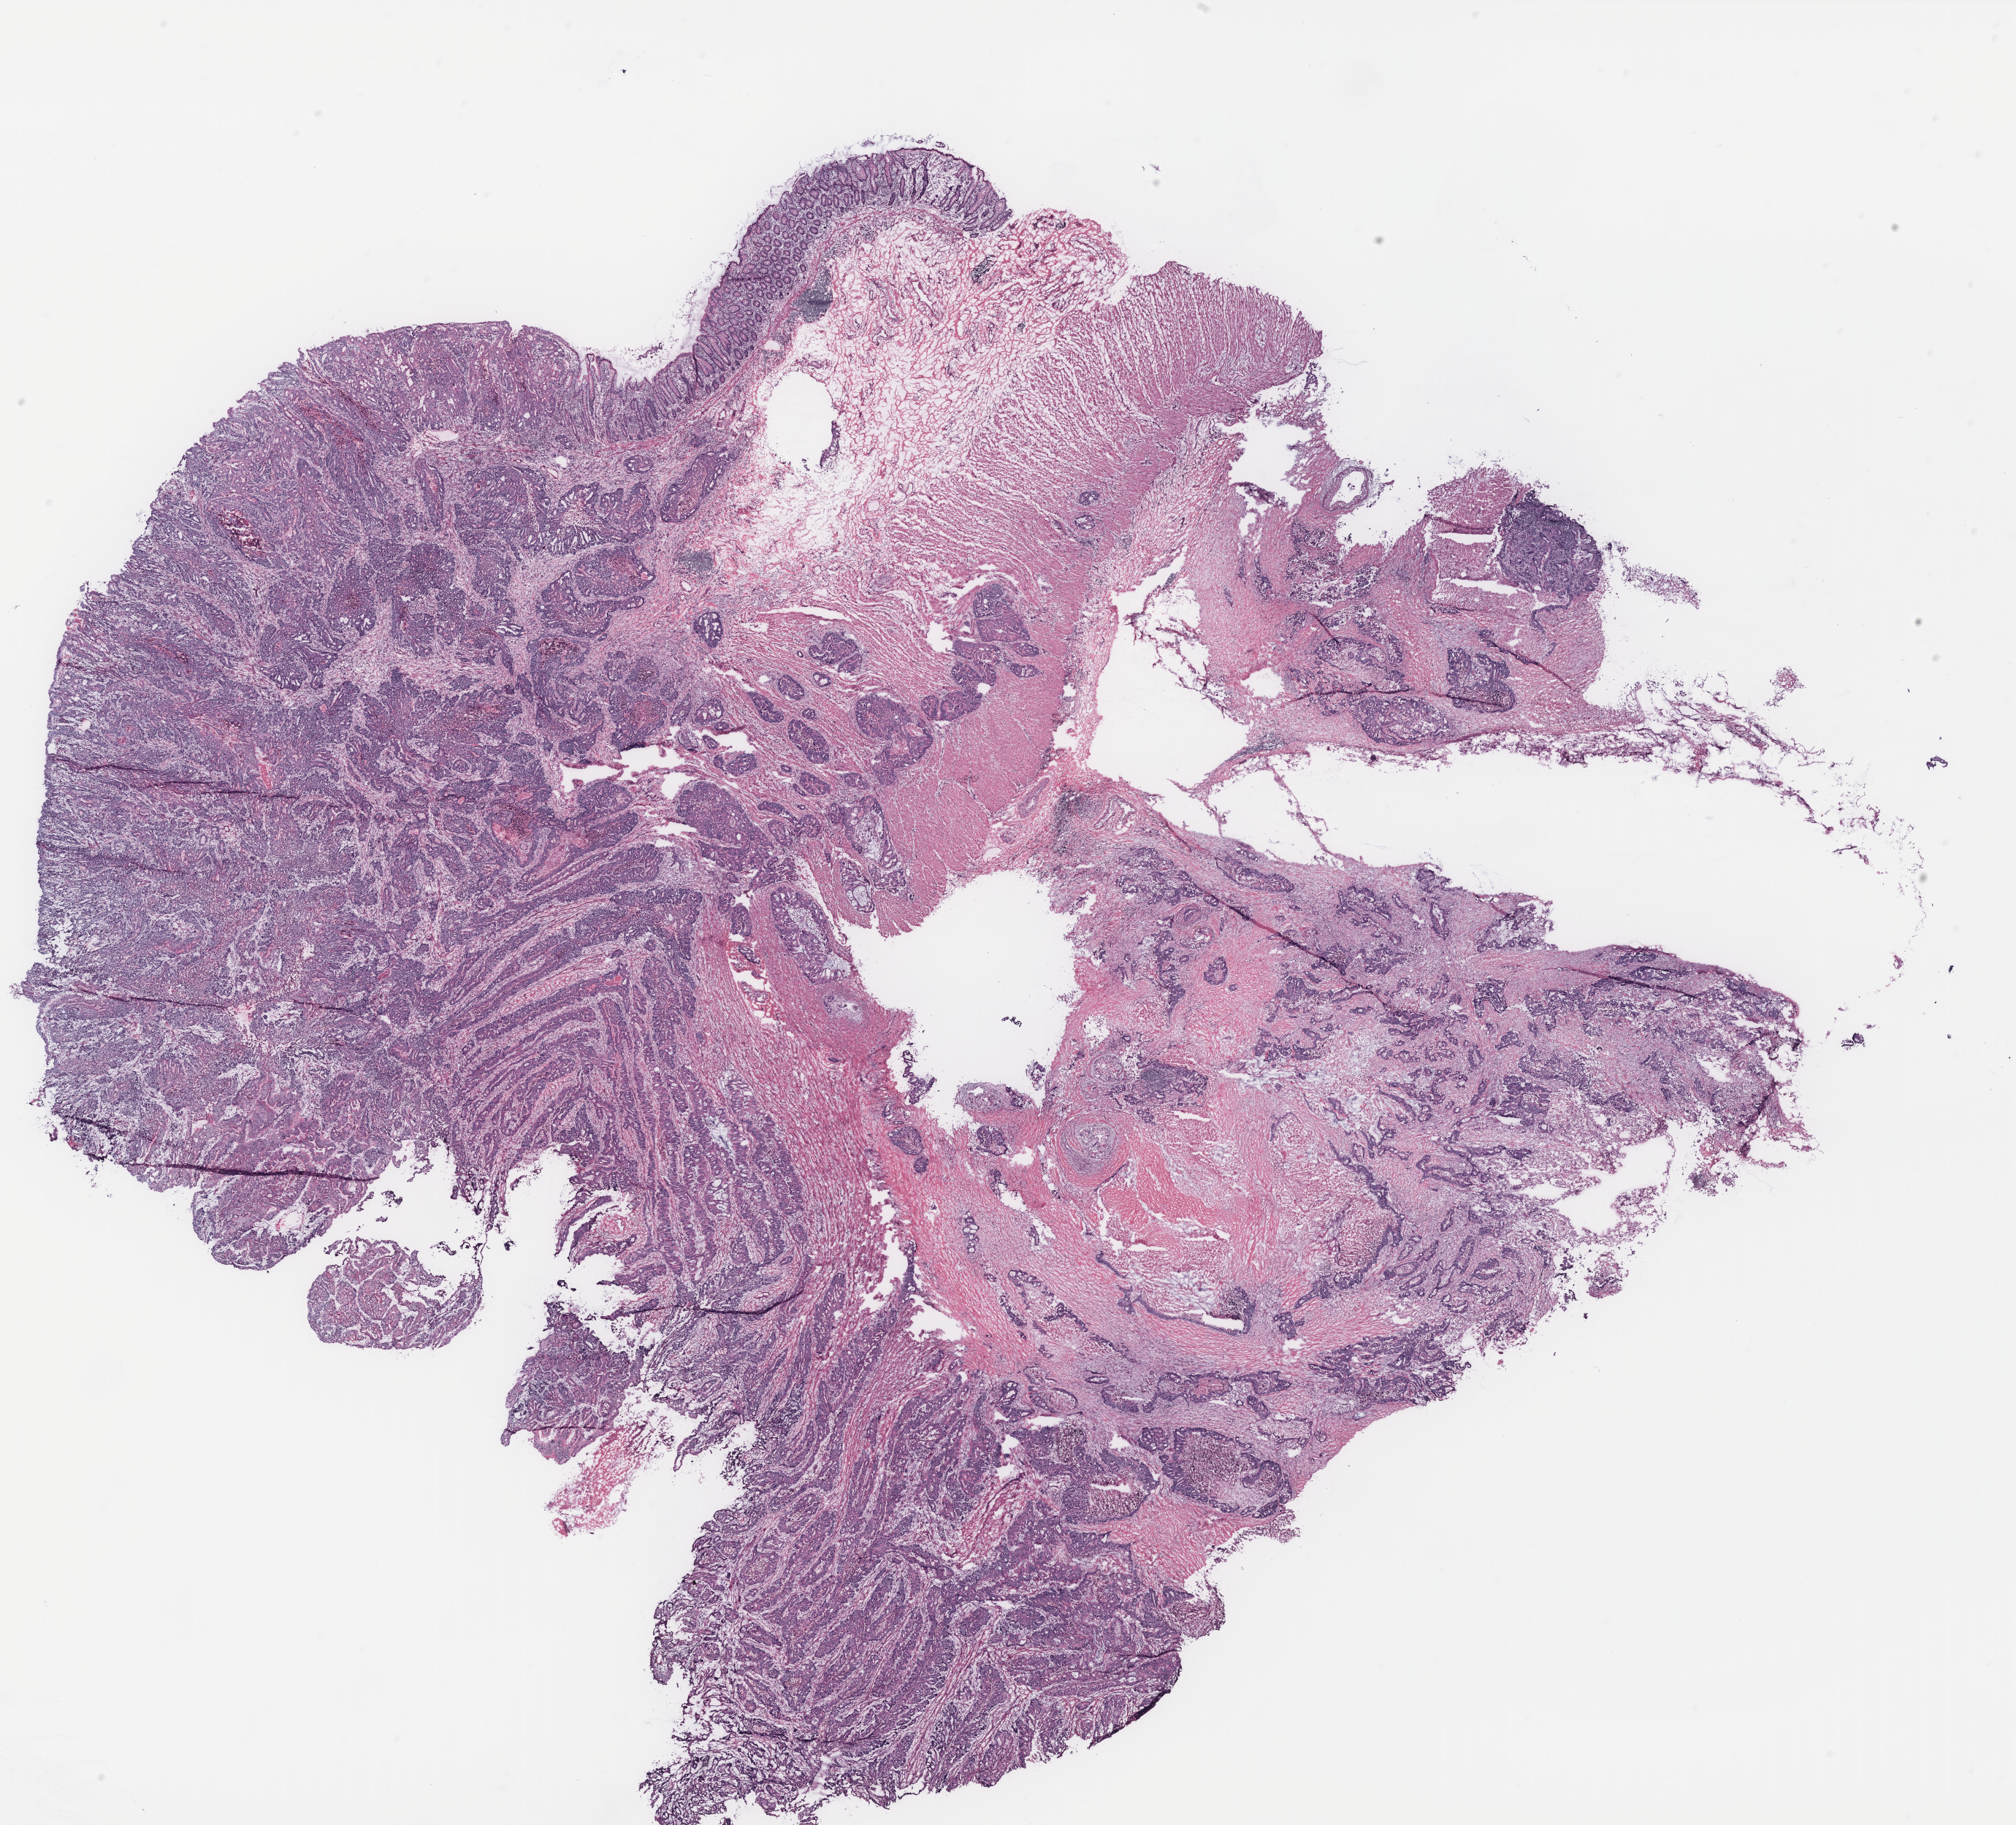
Digitized Hematoxylin and eosin (H&E) stained tissue section (whole slide), whole scanned area (about 22.1 x 20.0 mm, from a 40x scan) shown as a low-resolution overview. Colon, tissue type not recorded.
Patient diagnosis (cohort enrolment): colon cancer (colon).